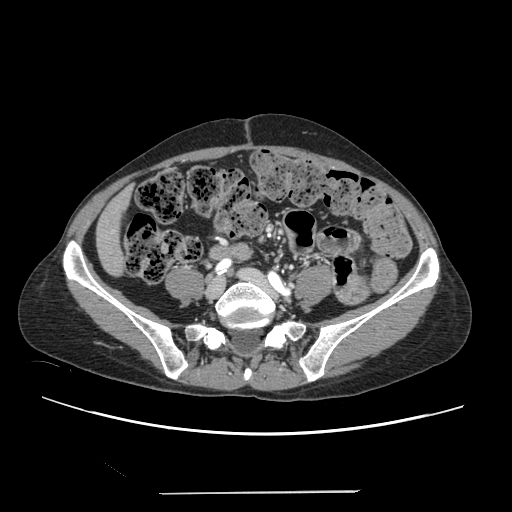
Contrast-enhanced abdominal CT, one axial slice. Position 18 of 240 along the scan axis. 120 kVp. Intravenous contrast given. Soft-tissue window (W 400 / L 40 HU). 1.25 mm slice thickness. 512 × 512 image matrix, field of view 371 × 371 mm. Female patient, age 60 years. From the clinical record (not read from this slice): diagnosis: colorectal cancer liver metastases, imaged before liver resection; multiple liver metastases: no; largest metastasis: 1.5 cm; disease in both lobes: no.
Outlined on this slice (manually delineated by an expert):
- liver: box from (x=98, y=191) to (x=130, y=274) px
- planned liver remnant (the part of the liver to remain after resection): (x=98, y=191)–(x=130, y=274)